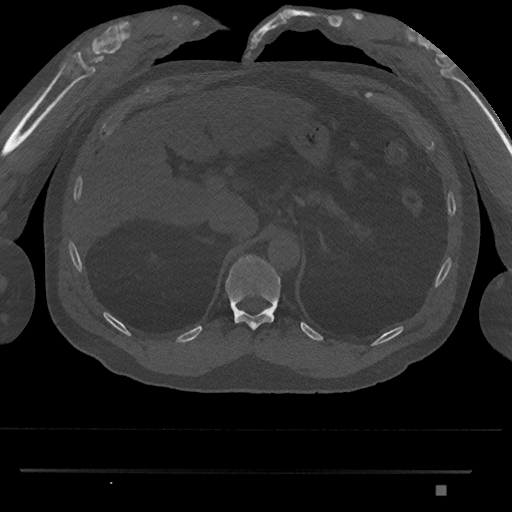
CT including the spine, one axial slice; position 944 of 1134 along the scan axis; 120 kVp; bone window (W 1800 / L 400 HU); 512 × 512 image matrix, field of view 429 × 429 mm. Patient: male, 65 years. From the clinical record (not read from this slice): primary cancer: prostate.
Structures marked on this image (semi-automatic segmentation, software-assisted and operator-edited):
- T11 vertebra: box from (x=225, y=254) to (x=281, y=330) px